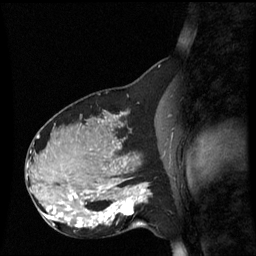
Breast MRI (dynamic contrast-enhanced), one sagittal slice; slice 31 of 60 in the series (ordered by position); dynamic contrast-enhanced series, image 2 of 3 at this slice position (ordered by acquisition); 1.5 T; TE 4.2 ms, TR 8.9 ms; 2.2 mm slice thickness; 256 × 256 image matrix, field of view 220 × 220 mm. Female patient, age 31 years. From the clinical record (not read from this slice): setting: breast cancer imaged before/during neoadjuvant chemotherapy; receptor status: HR-positive, HER2-negative.
Outlined on this slice (semi-automatically segmented with operator editing):
- analysis volume of interest (the breast-tissue region the enhancement analysis was run in; not a lesion): box from (x=90, y=180) to (x=152, y=231) px
- tumour enhancement mask (voxels above the 70 % enhancement threshold inside the analysis volume of interest): (x=90, y=184)–(x=152, y=227)